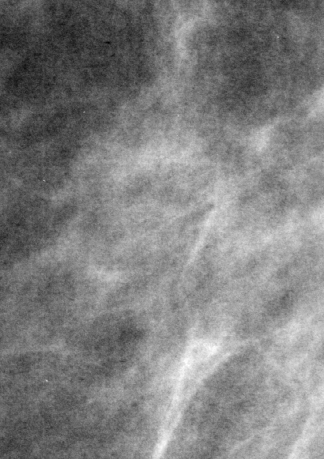
Cropped region of a digitized screen-film mammogram centred on a radiologist-marked abnormality, right breast, MLO view.
Marked abnormality: mass, shape focal asymmetric density; BI-RADS assessment category 3; benign without callback (not worked up further).